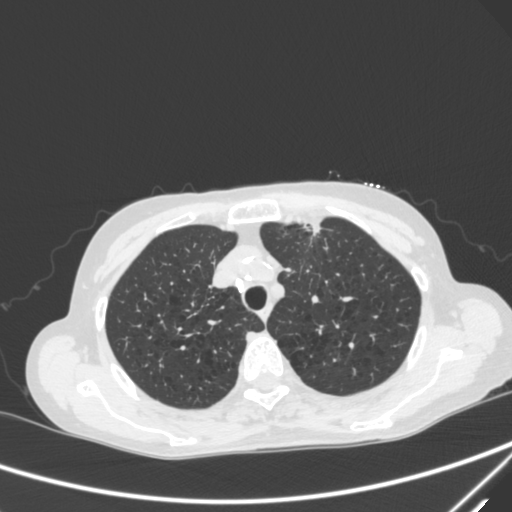
Chest CT, one axial slice. Position 238 of 300 along the scan axis. 120 kVp. Lung window (W 1500 / L -600 HU). 1 mm slice thickness. 512 × 512 image matrix, field of view 350 × 350 mm. Female patient, age 71 years. Case-level facts recorded for this patient, not image findings: clinical TNM (as recorded): T1c N0 M0.
Annotated regions visible in this slice (bounding box drawn by a radiologist):
- lung tumour (recorded histology: adenocarcinoma): bounding box (x1, y1, x2, y2) in pixels: (303, 219, 331, 240)